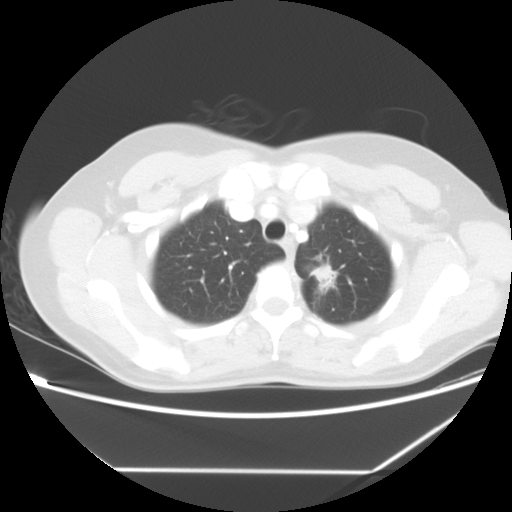
Chest CT, one axial slice. Slice 49 of 60 in the series (ordered by position). Lung window (W 1500 / L -600 HU). 5 mm slice thickness. 512 × 512 image matrix, field of view 367 × 367 mm. Patient: female, 43 years. From the clinical record (not read from this slice): clinical TNM (as recorded): T1c N0 M1b.
Structures marked on this image (bounding box drawn by a radiologist):
- lung tumour (recorded histology: adenocarcinoma): bounding box (x1, y1, x2, y2) in pixels: (312, 265, 340, 299)